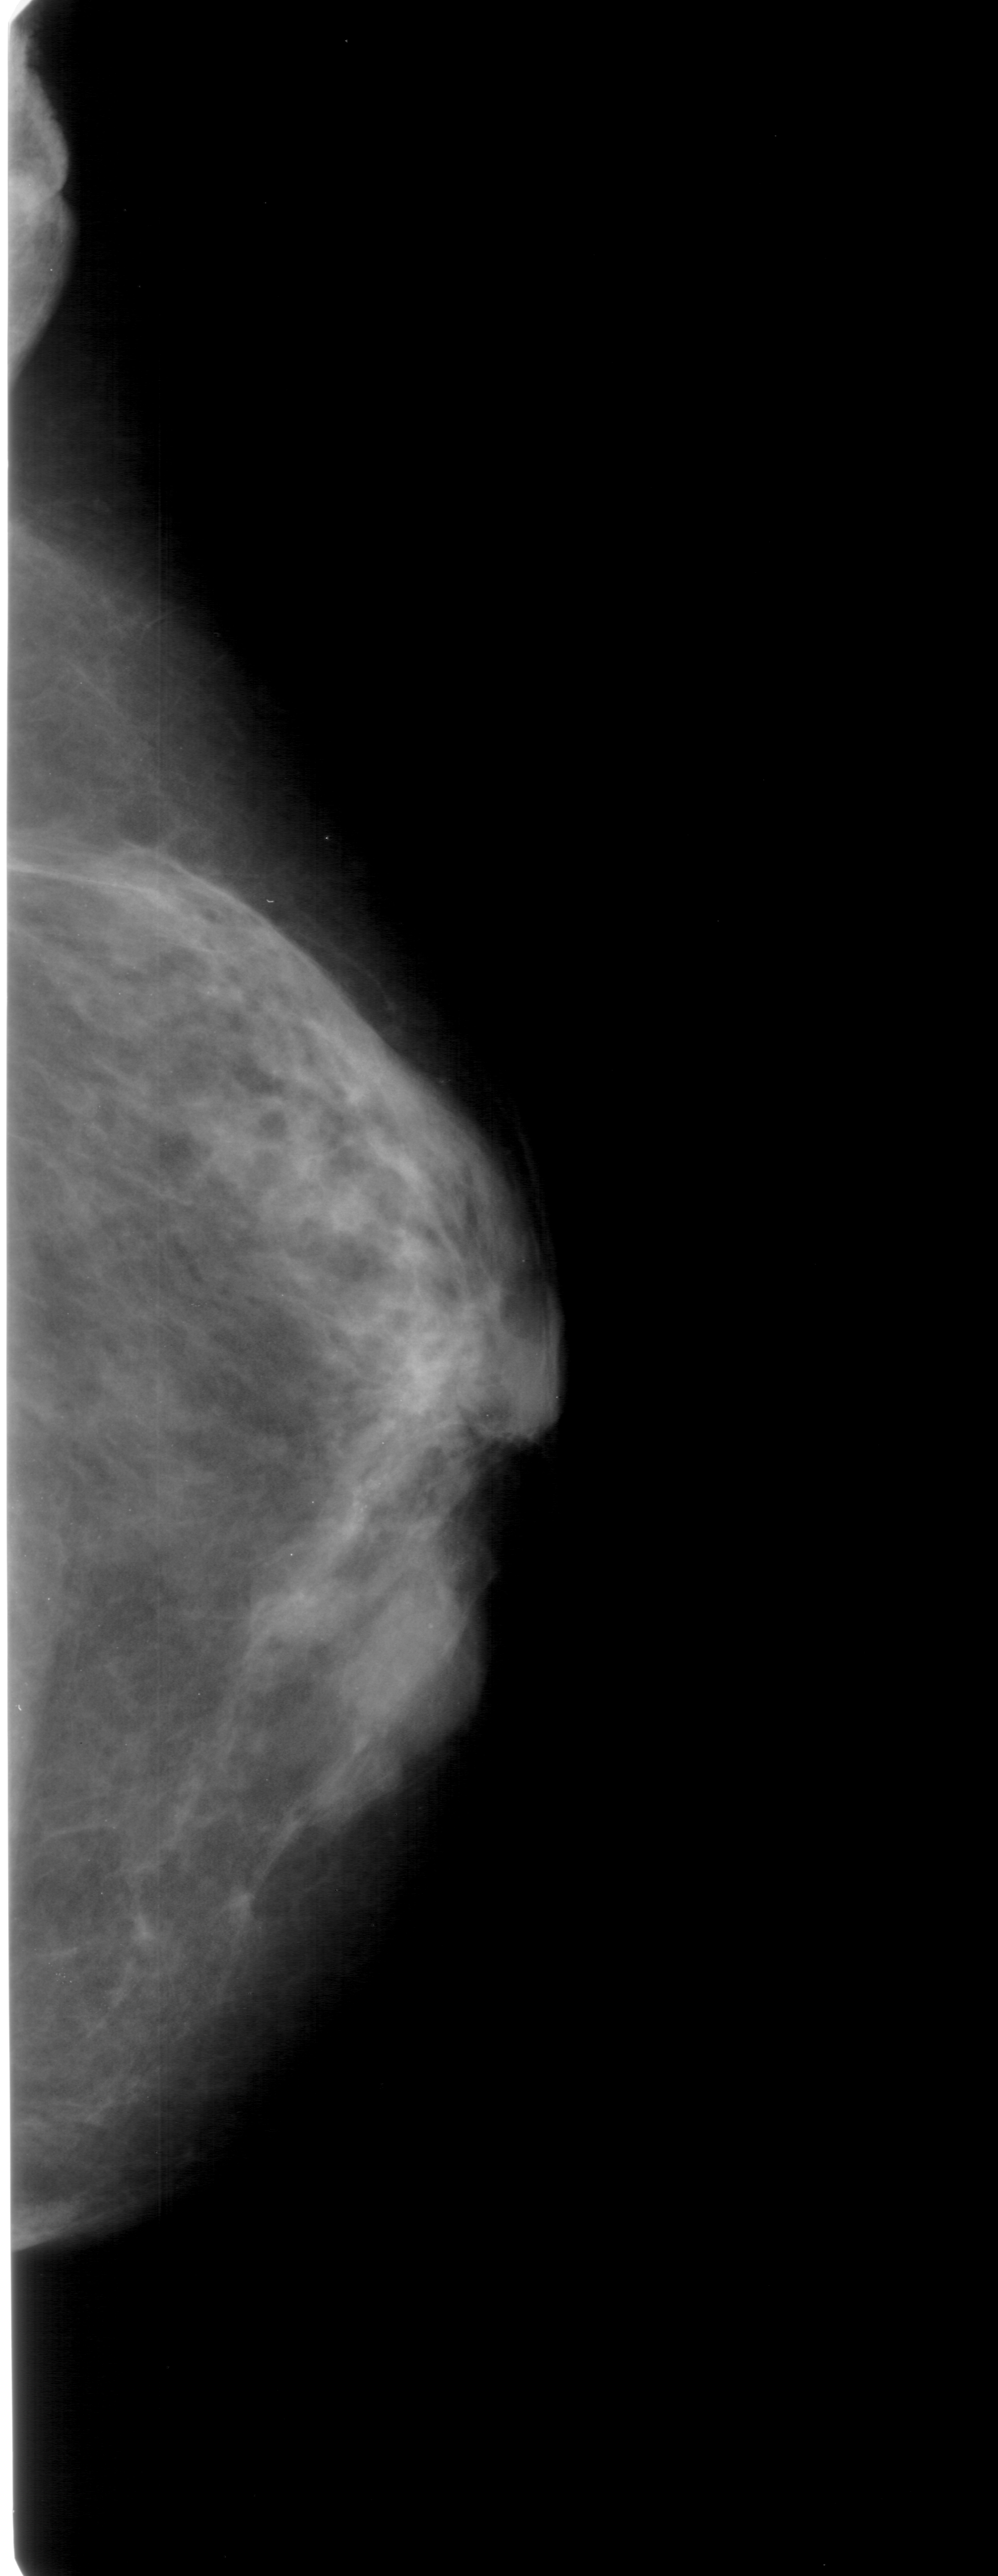
Digitized screen-film mammogram, right breast, craniocaudal (CC) view.
Finding: calcifications, morphology pleomorphic, distribution clustered; BI-RADS assessment category 4; pathology result (as recorded, not read from the image): malignant.